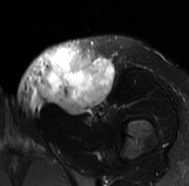
MRI of an extremity soft-tissue mass, one axial slice; position 33 of 77 along the scan axis; T2-weighted fat-saturated; MR volume resampled by the dataset authors to the PET/CT grid (not the native acquisition matrix); 189 × 186 image matrix, field of view 185 × 182 mm. Female patient. Case-level facts recorded for this patient, not image findings: histological type: leiomyosarcoma; grade: high; site of the primary tumour: groin.
Outlined on this slice (expert contour drawn on MRI and transferred to this co-registered scan by the dataset authors):
- gross tumour volume including surrounding oedema: bounding box <15,36,114,119> (left, top, right, bottom; pixels)
- gross tumour volume (mass): <38,47,114,114>